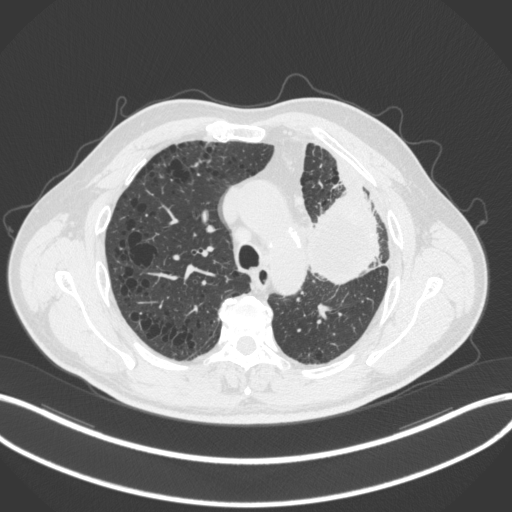
Chest CT, one axial slice. Slice 210 of 286 in the series (ordered by position). 120 kVp. Lung window (W 1500 / L -600 HU). 512 × 512 image matrix, field of view 400 × 400 mm. Patient: male, 68 years. Case-level facts recorded for this patient, not image findings: clinical TNM (as recorded): T3 N3 M1.
Structures marked on this image (bounding box drawn by a radiologist):
- lung tumour (recorded histology: adenocarcinoma): bounding box (x1, y1, x2, y2) in pixels: (305, 192, 386, 290)